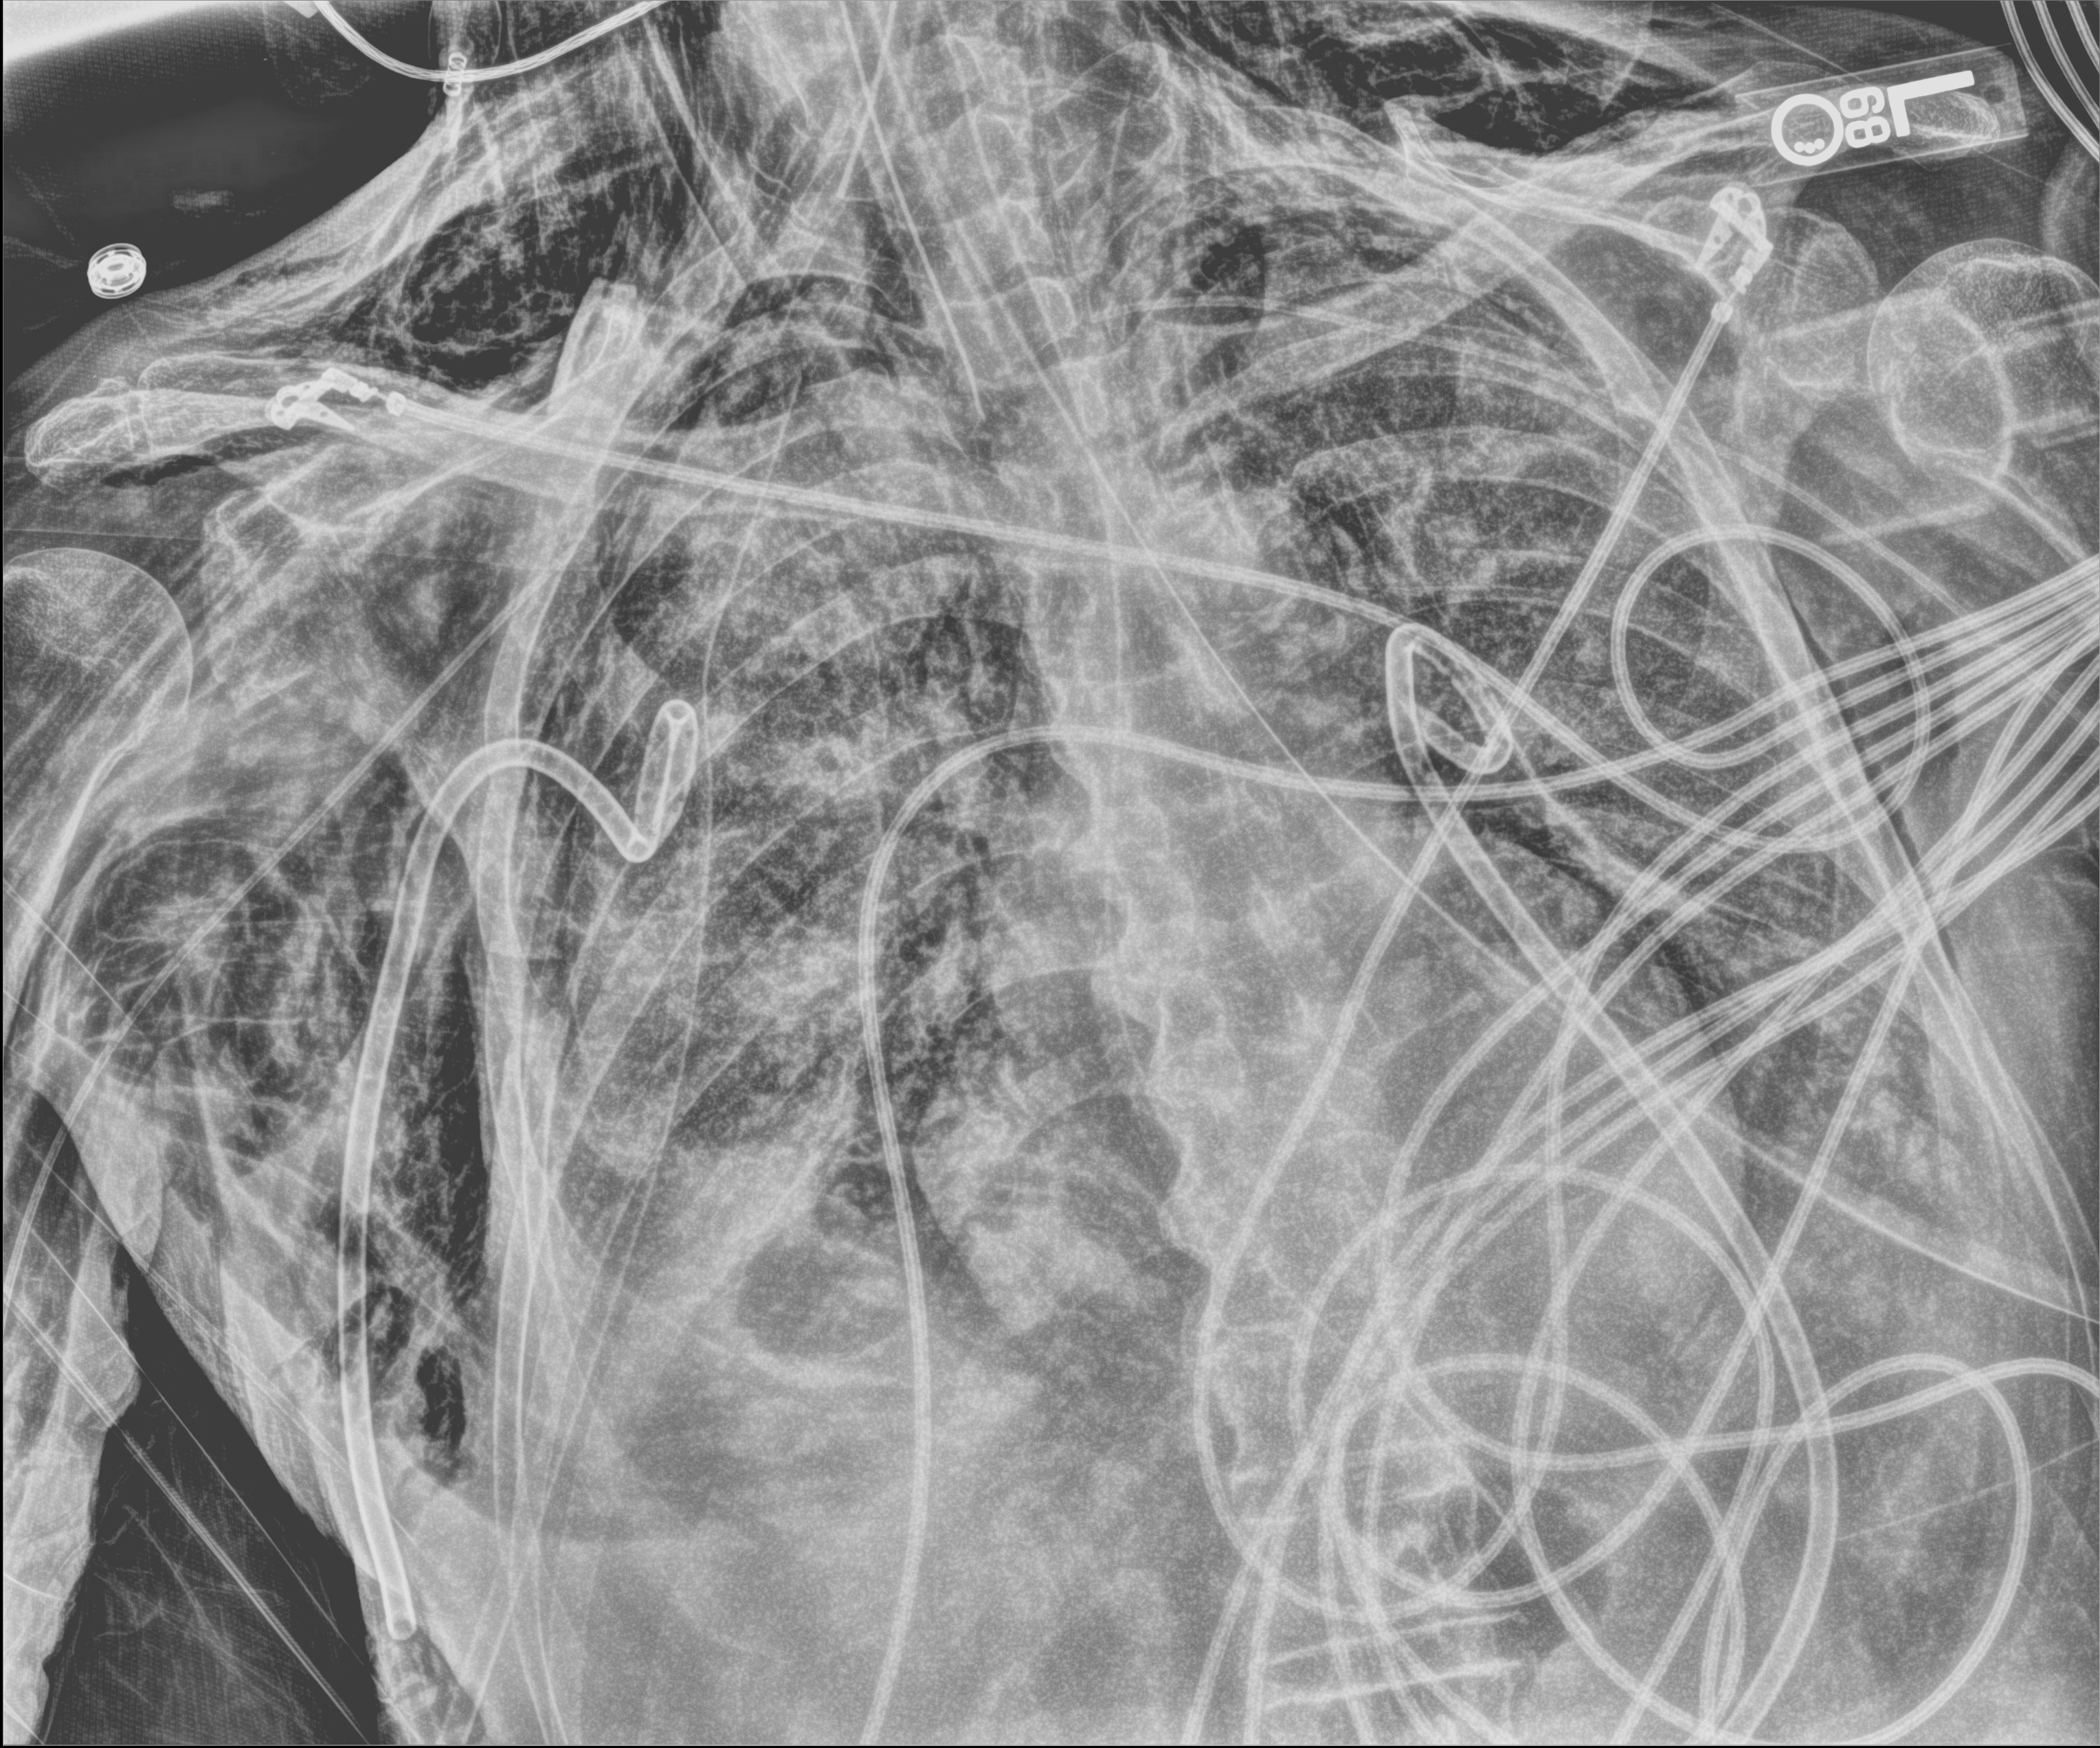
Bedside chest radiograph (computed radiography); anteroposterior (AP) projection. Male patient hospitalised with COVID-19, age 75–90 years.
From the hospital-stay record, not from the radiograph (when in the stay this image was taken is not recorded):
- hypertension (admission record): yes